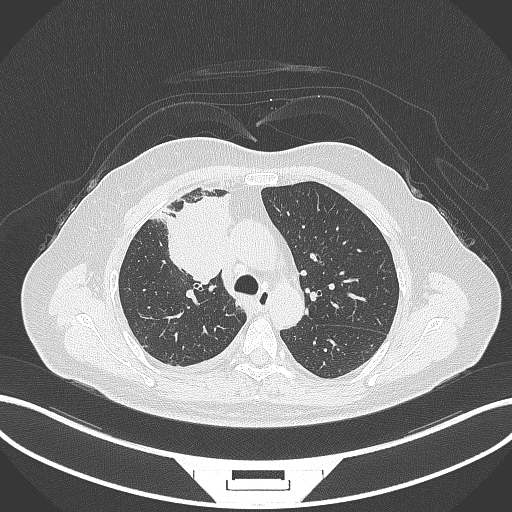
Chest CT, one axial slice; position 198 of 305 along the scan axis; reconstruction kernel B70f; 120 kVp; lung window (W 1500 / L -600 HU); 512 × 512 image matrix, field of view 400 × 400 mm. Patient: female, 52 years. From the clinical record (not read from this slice): clinical TNM (as recorded): T3 N1 M1.
Structures marked on this image (rectangle marked by the reading radiologist):
- lung tumour (recorded histology: adenocarcinoma): bounding box <149,191,236,287> (left, top, right, bottom; pixels)